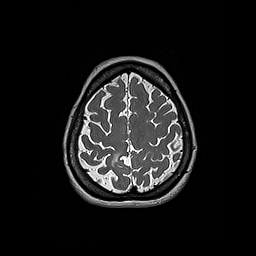
Brain MRI from a brain-tumour surgery series, one axial slice; position 51 of 192 along the scan axis; 256 × 256 image matrix, field of view 250 × 250 mm. Case-level facts recorded for this patient, not image findings: histopathology: Oligodendroglioma; WHO grade: 2; IDH mutation: yes; tumour location: Right Parietal.
Annotated regions visible in this slice (manually delineated by an expert):
- tumour: bounding box (x1, y1, x2, y2) in pixels: (111, 152, 120, 167)